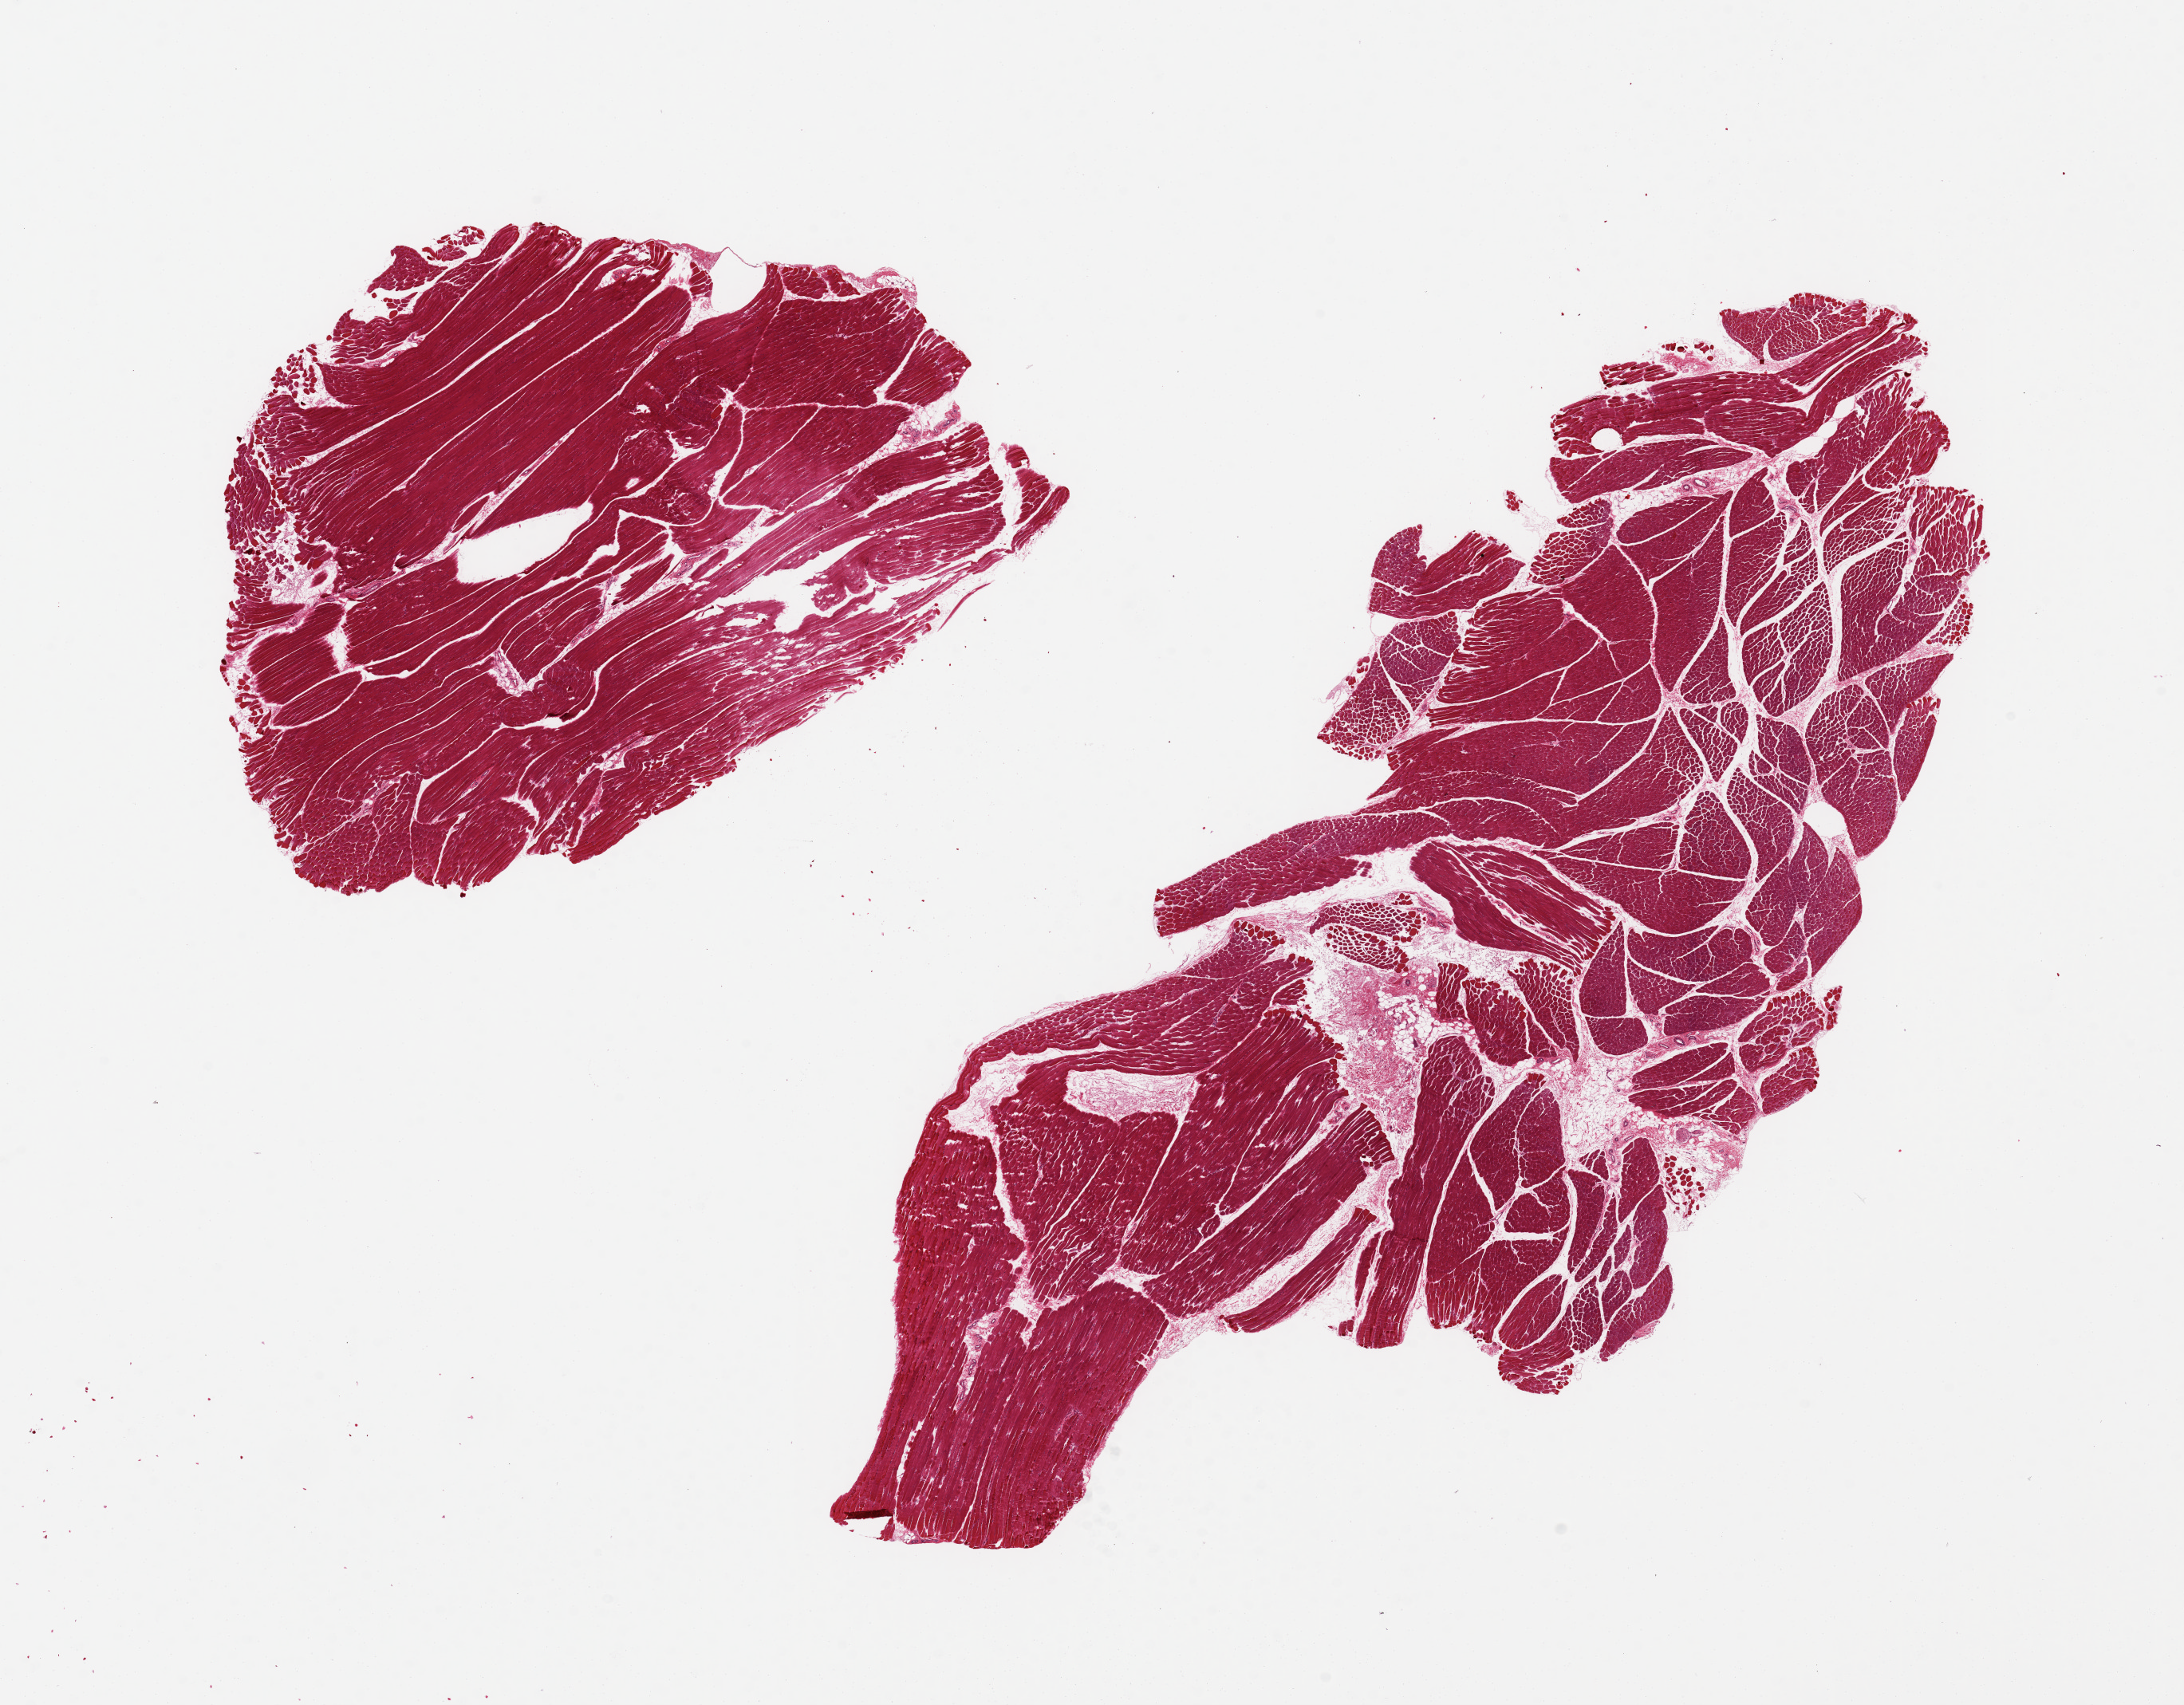
Digitized hematoxylin and eosin (H&E)-stained section — shown as a low-resolution overview of the whole scanned area (about 21.7 x 16.9 mm), PAXgene-fixed paraffin-embedded (PFPE) section, target tissue: skeletal muscle, donor tissue sample.
Pathologist's review note for this sample: 2 pieces ~10x7mm, <5% interstital fat.